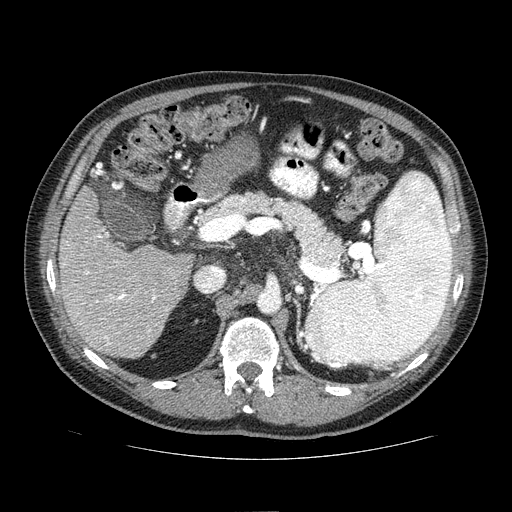
Contrast-enhanced abdominal CT (liver protocol), one axial slice. Slice 34 of 81 in the series (ordered by position). Reconstruction kernel STANDARD. 100 kVp. One of 2 acquisitions stored at this slice position. Soft-tissue window (W 400 / L 40 HU). 512 × 512 image matrix, field of view 400 × 400 mm. Case-level facts recorded for this patient, not image findings: diagnosis: hepatocellular carcinoma (patient treated with transarterial chemoembolisation; whether this scan precedes or follows treatment is not stated here); TNM stage (as recorded): Stage-IIIA; Child-Pugh class: A; tumour differentiation: well differentiated.
Outlined on this slice (semi-automatically segmented with operator editing):
- liver parenchyma outside the tumour (the mass and vessels are separate outlines, so this box may not span the whole liver): bounding box [x1, y1, x2, y2] px = [58, 186, 194, 358]
- liver vessels: [81, 233, 157, 346]